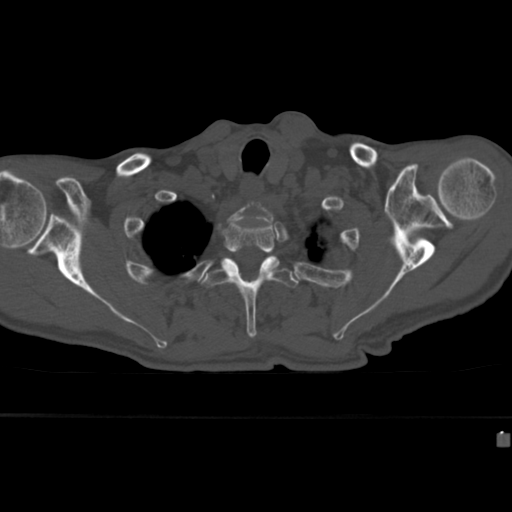
CT including the spine, one axial slice; position 339 of 430 along the scan axis; bone window (W 1800 / L 400 HU); 1.5 mm slice thickness; 512 × 512 image matrix. Patient: male, 64 years. Case-level facts recorded for this patient, not image findings: primary cancer: uterus; vertebrae with lytic lesions (as recorded): T1, T4, T5, T7, L5.
Annotated regions visible in this slice (semi-automatically segmented with operator editing):
- T2 vertebra: box from (x=223, y=217) to (x=280, y=281) px
- T3 vertebra: (x=201, y=256)–(x=299, y=339)